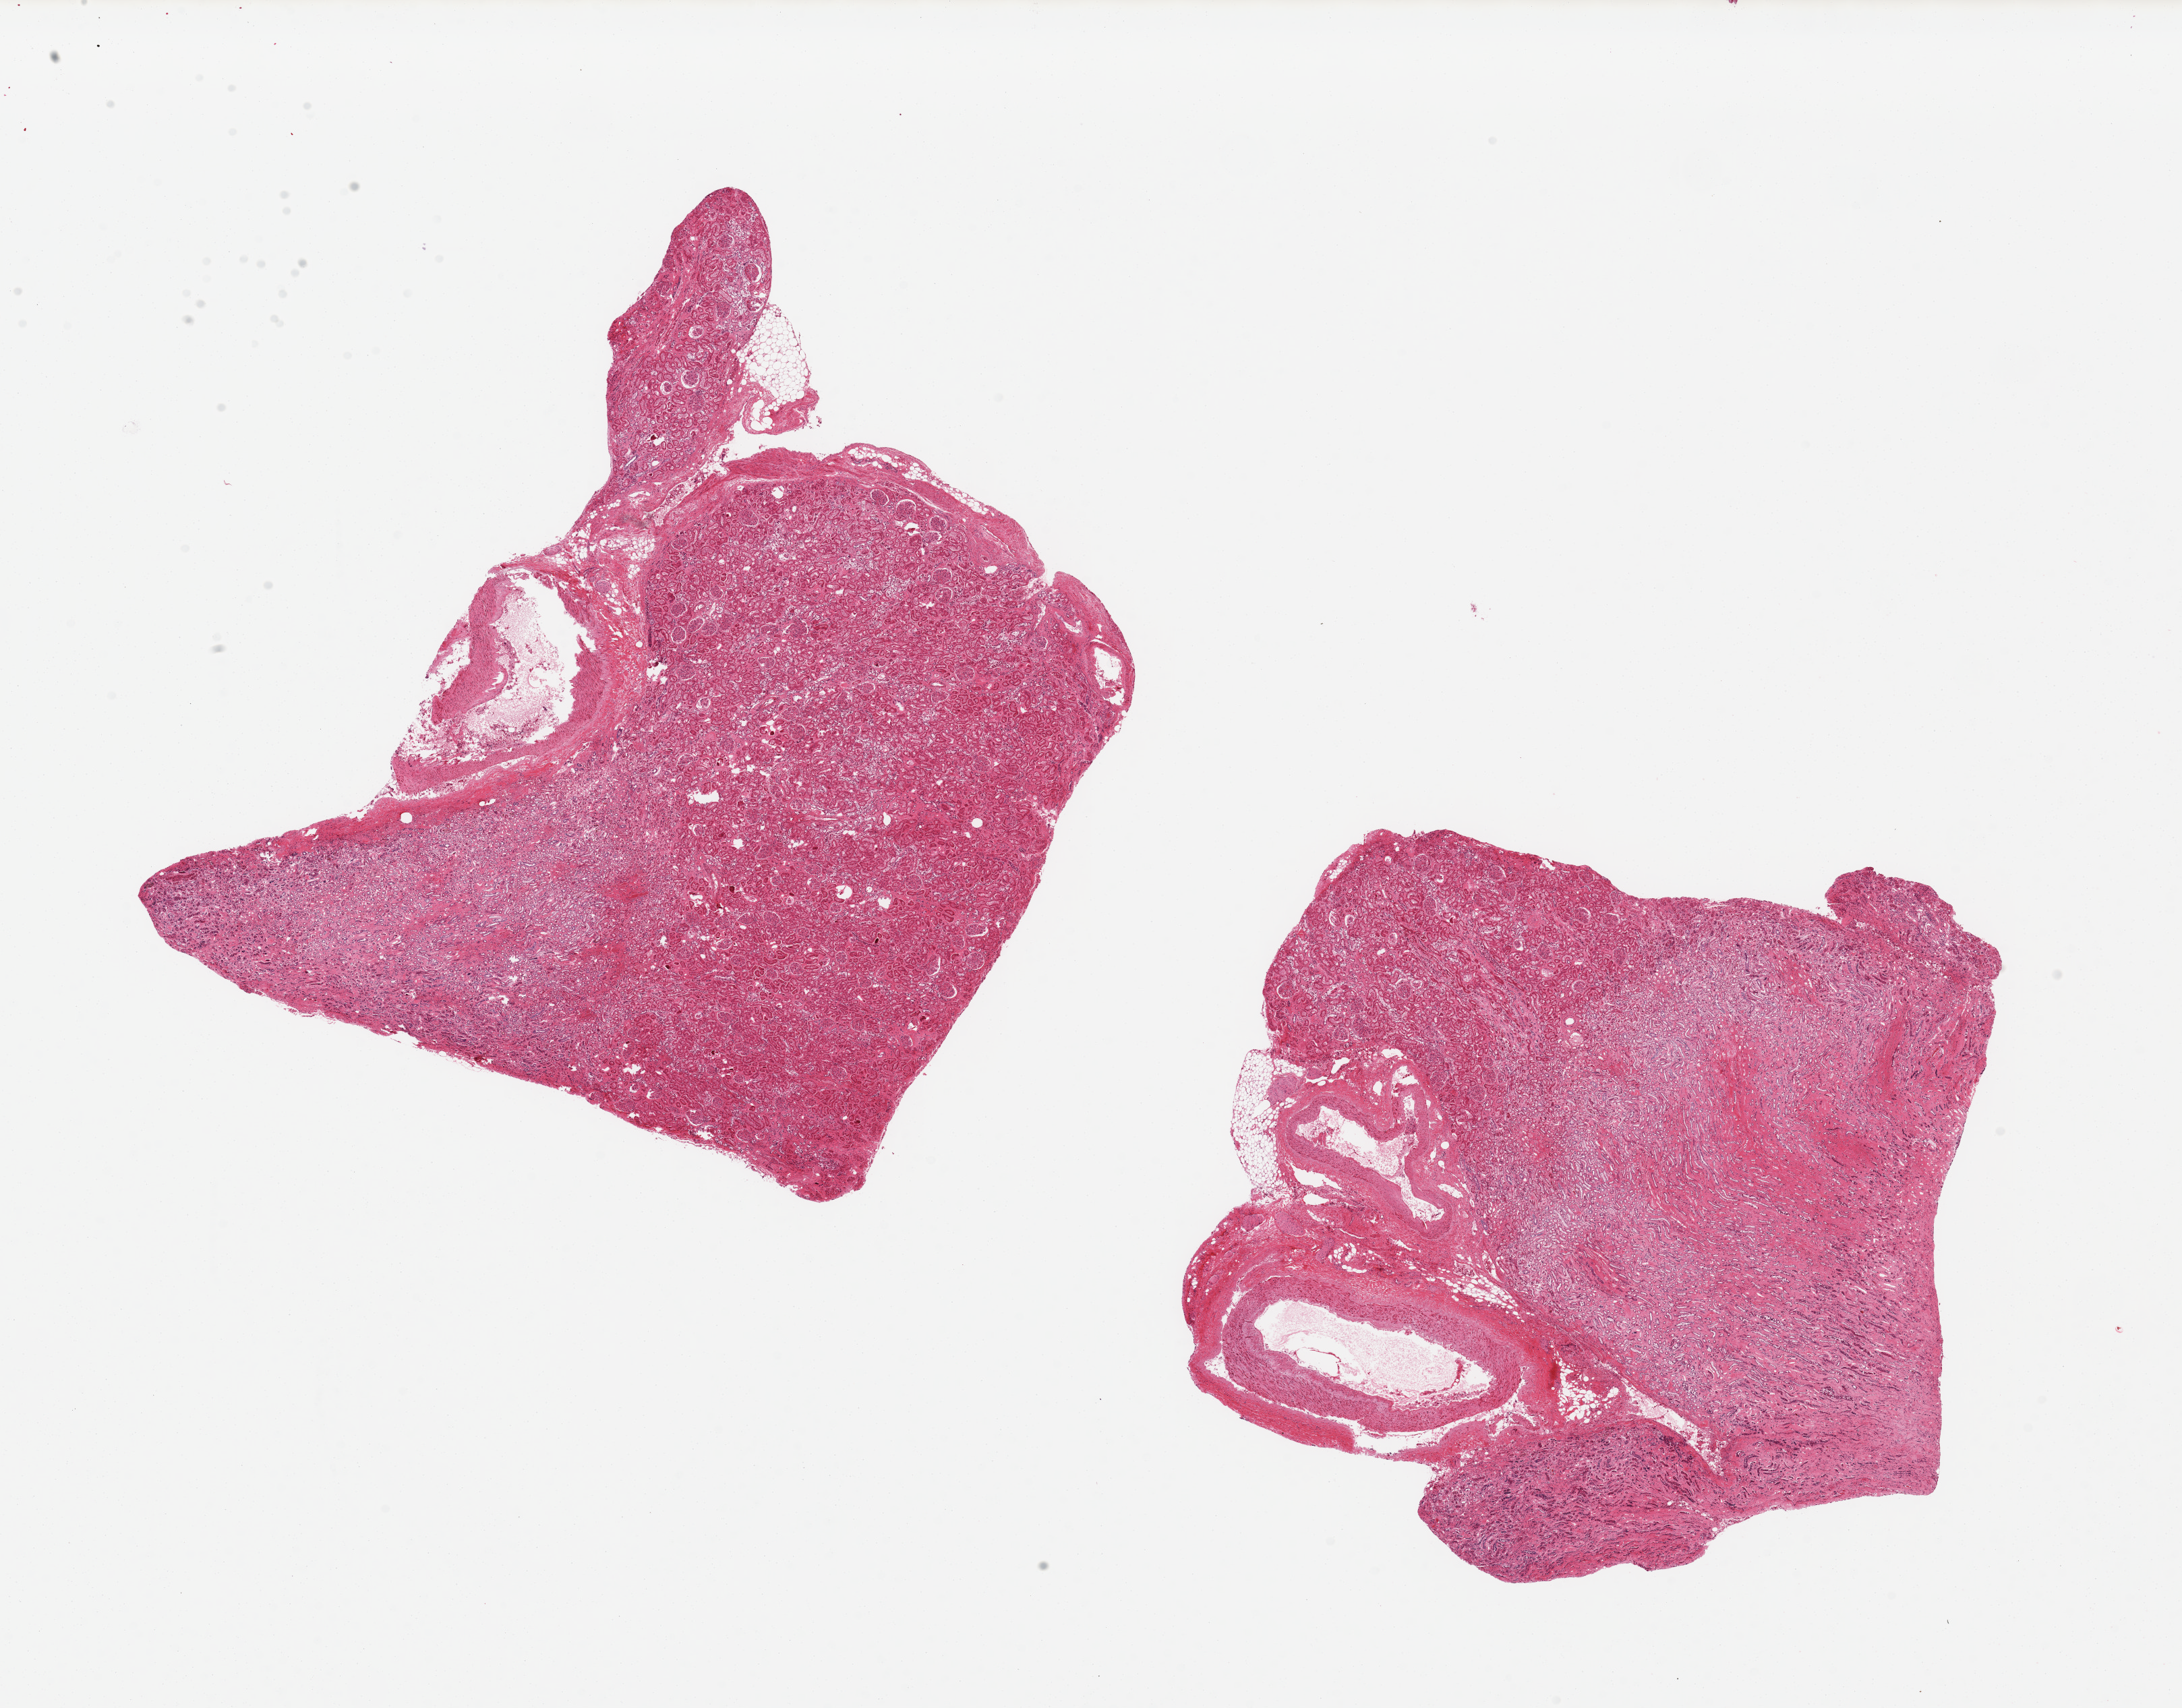
Digitized H&E-stained section, brightfield — whole scanned area (about 25.6 x 20.0 mm) shown as a low-resolution overview. PAXgene-fixed paraffin-embedded (PFPE) section. Sampled site (target tissue): renal medulla. Donor tissue sample. Female donor.
* pathologist's review note for this sample: 2 pieces, 8x8 & 9x8 mm; both contain medulla and cortex (image)